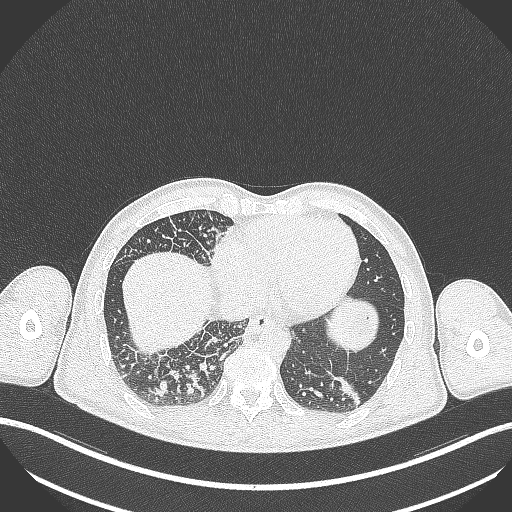
Chest CT, one axial slice; position 83 of 348 along the scan axis; reconstruction kernel B70f; 120 kVp; lung window (W 1500 / L -600 HU); 1 mm slice thickness; 512 × 512 image matrix, field of view 400 × 400 mm. Patient: male, 49 years. Case-level facts recorded for this patient, not image findings: clinical TNM (as recorded): T2b N1 M0.
Outlined on this slice (rectangle marked by the reading radiologist):
- lung tumour (recorded histology: adenocarcinoma): box from (x=334, y=372) to (x=364, y=410) px